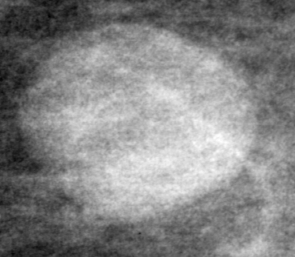
Crop from a digitized film mammogram around one marked abnormality, left breast, MLO view, BI-RADS breast density category 2 (scale 1–4).
- Marked abnormality: mass, shape round, margins circumscribed; BI-RADS assessment category 3; pathology (as recorded): benign.